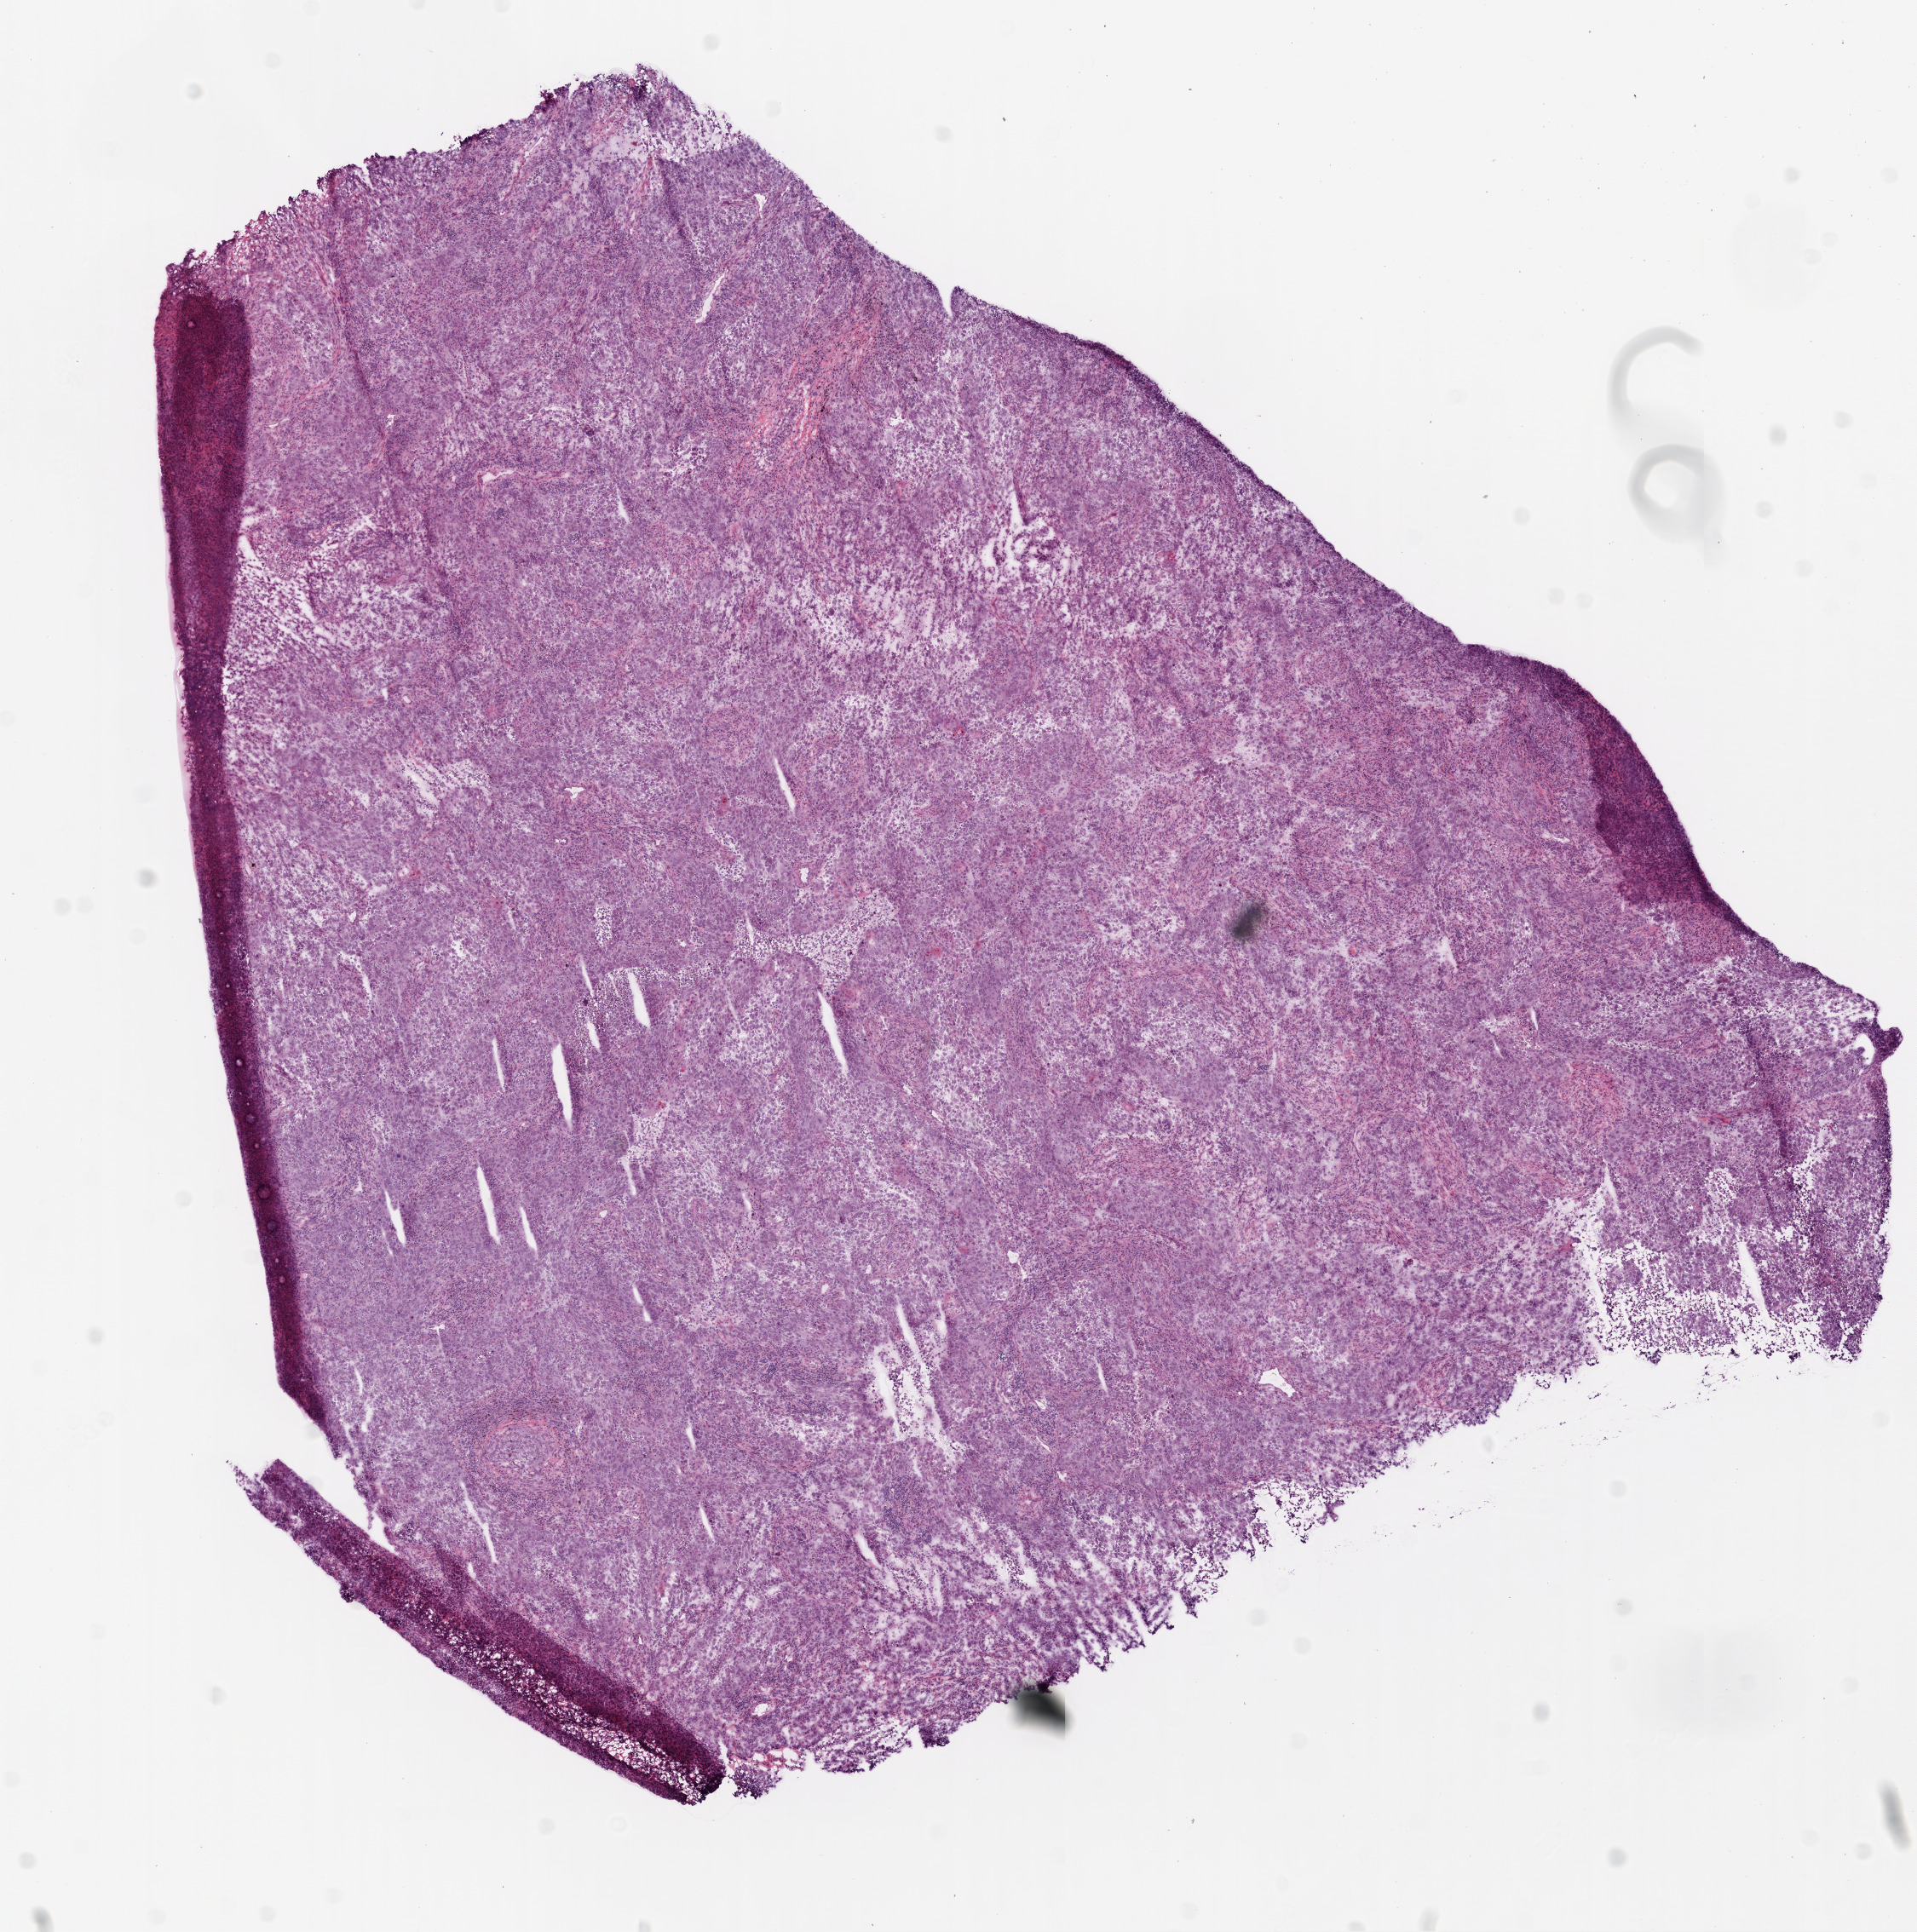
Whole-slide histology image, Hematoxylin and eosin (H&E) stained — low-resolution overview of the scanned area, about 9.0 x 9.1 mm (from a 20x scan). Frozen section from the bottom of the tissue portion. Sample: primary tumour, lung. Male, age 63 years at initial diagnosis. Composition of this section per pathologist review: tumour cells 83%, tumour nuclei 80%, normal cells 0%, stromal cells 5%, necrosis 12%.
* AJCC pathologic stage: IB (5th edition)
* laterality: right
* TNM: T2 N0 M0
* pathologic diagnosis: Squamous cell carcinoma, NOS (upper lobe, lung)